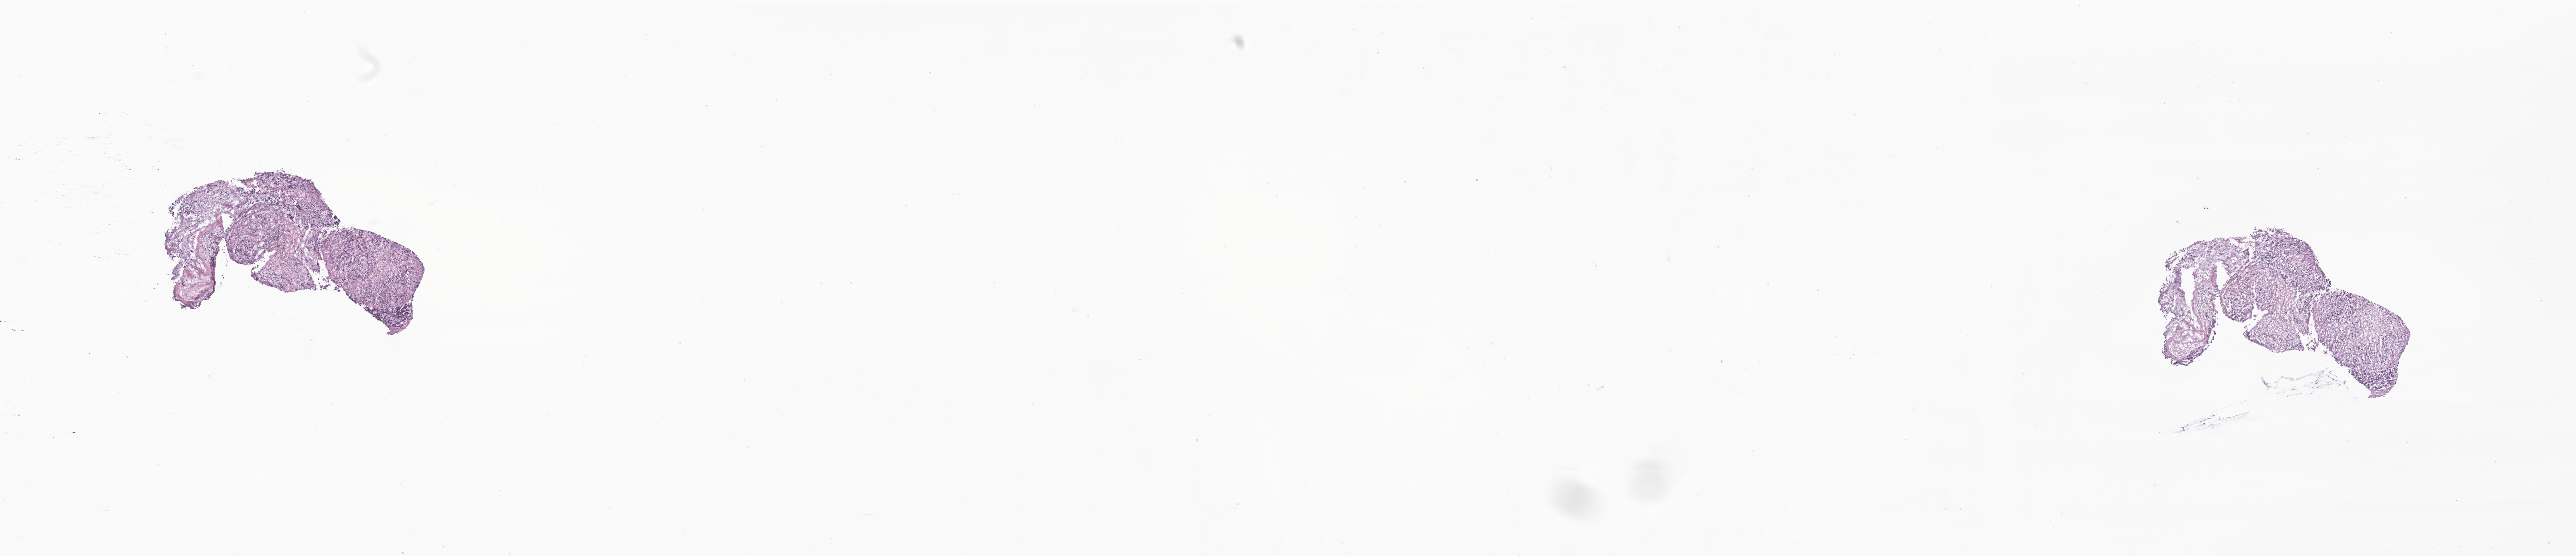
Haematoxylin and eosin whole-slide image of tumor tissue from the adrenal gland, a low-resolution overview of the entire scanned area, about 30.4 x 6.6 mm. Cryosection (OCT / tissue freezing medium). Male patient, age 381 days (about 1.0 years).
- recorded diagnosis: Neuroblastoma, NOS